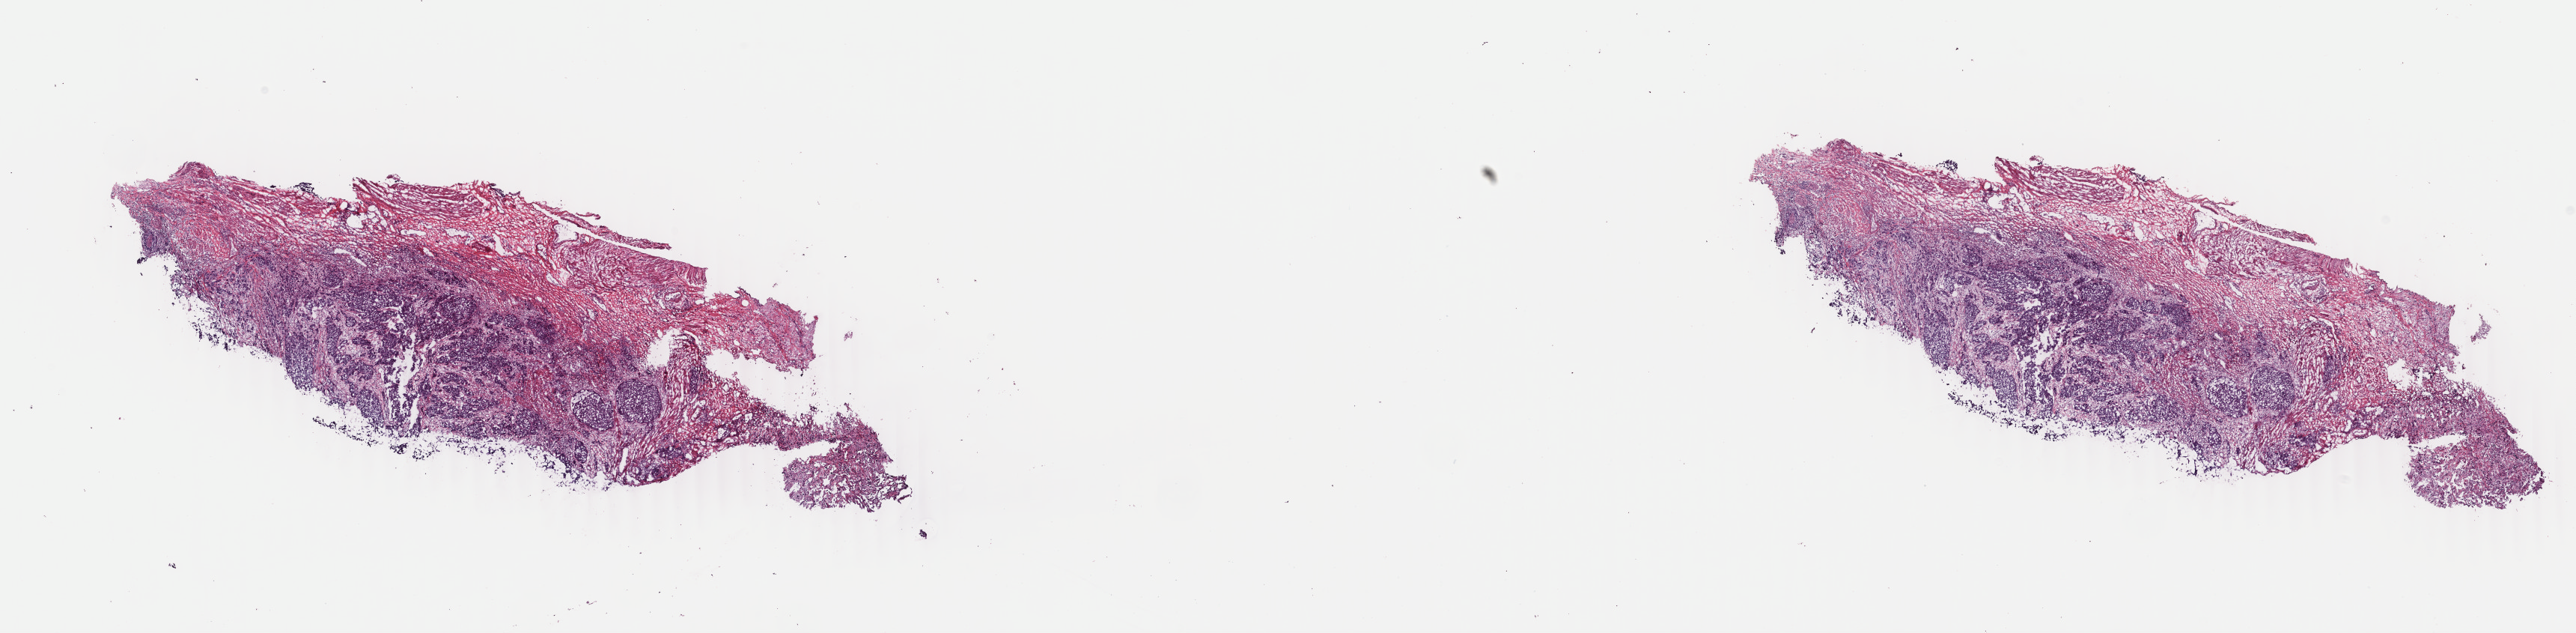
Whole-slide histology image, H&E, shown as a low-resolution overview of the whole scanned area (about 27.4 x 6.7 mm, slide scanned at 40x); frozen section from the top of the tissue portion; primary tumour sample from the bladder. Male, age 81 years at initial diagnosis. Pathologist review of this section (percent, as recorded): tumour cells 70%, tumour nuclei 70%.
Diagnosis: Transitional cell carcinoma (trigone of bladder).